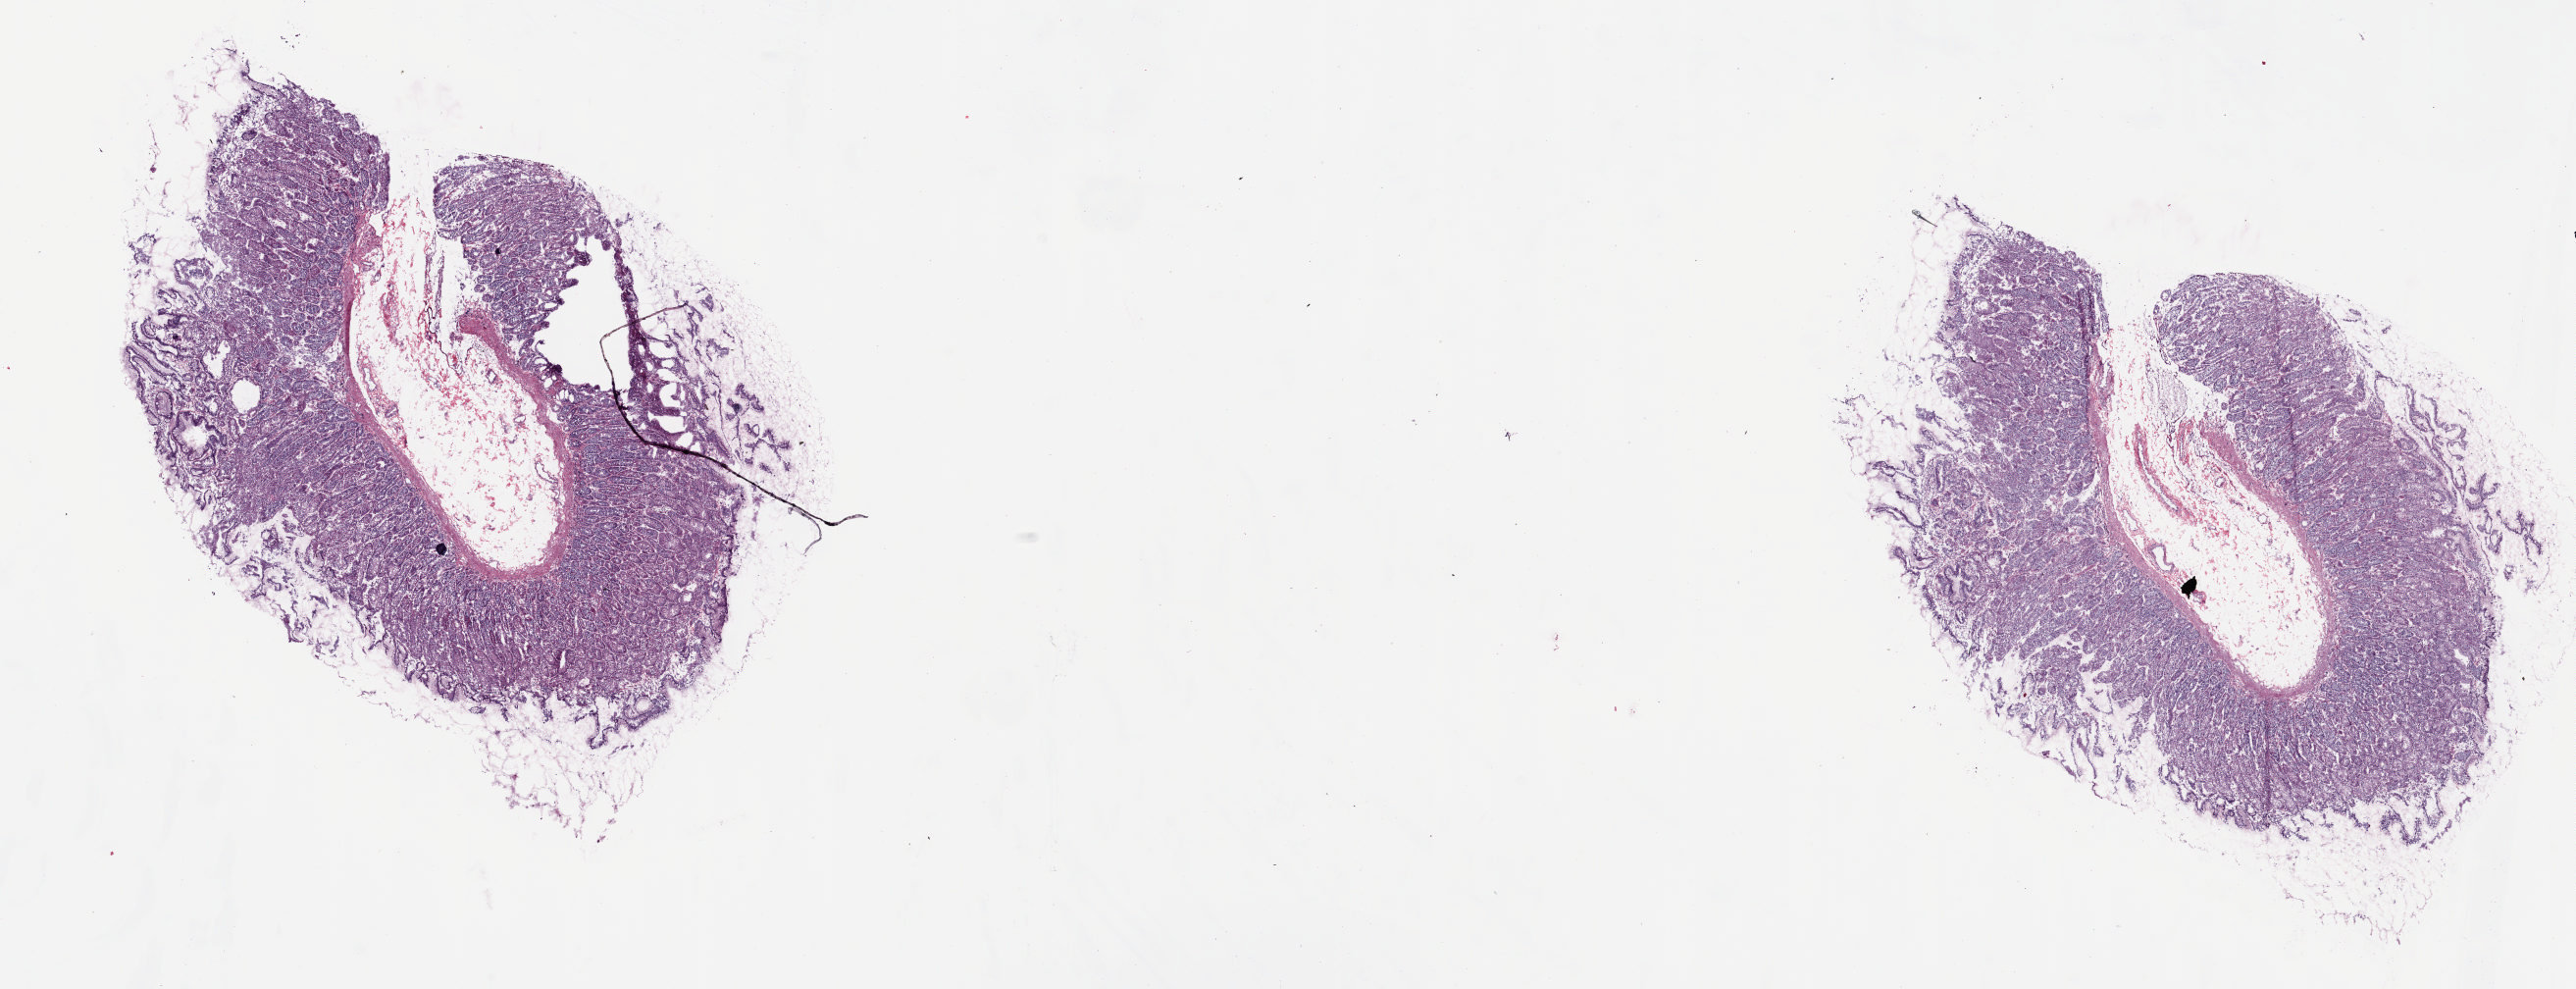
Digitized Hematoxylin and eosin (H&E) stained tissue section (whole slide), low-resolution overview of the scanned area, about 20.8 x 8.0 mm (from a 20x scan); frozen section from the top of the tissue portion; sample: solid tissue normal (non-tumour tissue), esophagus. Female, age 67 years at initial diagnosis. Pathologist review of this section (percent, as recorded): tumour cells 0%, tumour nuclei 0%, normal cells 100%, stromal cells 0%, necrosis 0%. Inflammatory infiltration, as recorded: lymphocyte infiltration 2%, monocyte infiltration 0%, neutrophil infiltration 0%.
This section: solid tissue normal sample (biorepository sample class). Patient diagnosis: Adenocarcinoma, NOS (lower third of esophagus).